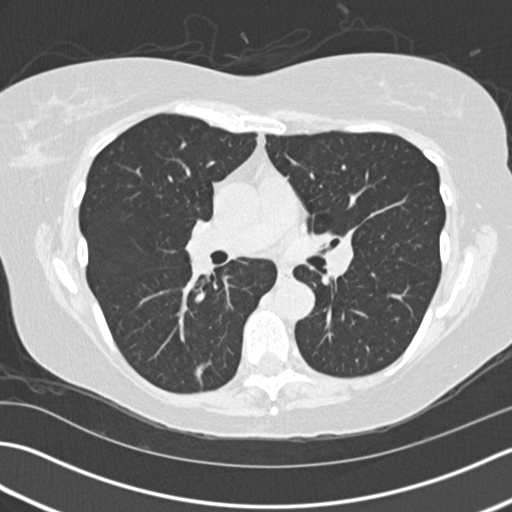
Axial slice from a low-dose chest CT screening exam. Third screening round (two years after baseline). Lung window (W 1500 / L -600 HU). Female, age 60 years at enrolment. Former smoker at enrolment.
Expert reader's lesion annotation, bounding box <179,351,225,395> (left, top, right, bottom; pixels). The screening reader recorded 3 non-calcified nodules or masses ≥4 mm on this exam; which of them this box marks is not recorded. Official screen result: positive, other. Participant outcome: lung cancer diagnosed 68 days after this screen — acinar cell carcinoma, right lower lobe, moderately differentiated (G2), stage IA (AJCC 6th edition), 10 mm at pathology.